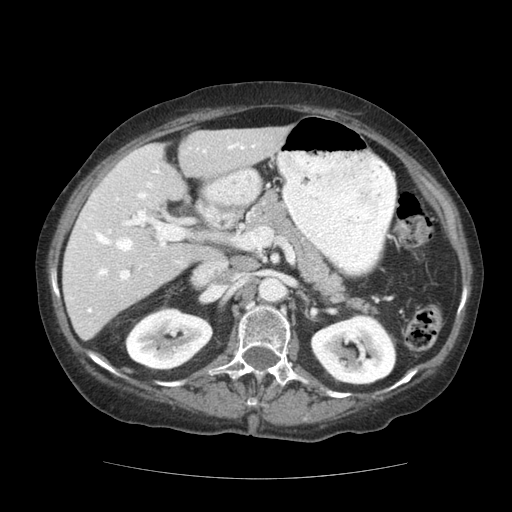
Contrast-enhanced abdominal CT (liver protocol), one axial slice. Position 67 of 111 along the scan axis. 140 kVp. Soft-tissue window (W 400 / L 40 HU). 2.5 mm slice thickness. 512 × 512 image matrix. From the clinical record (not read from this slice): diagnosis: hepatocellular carcinoma (patient treated with transarterial chemoembolisation; whether this scan precedes or follows treatment is not stated here); TNM stage (as recorded): Stage-I; Child-Pugh class: A; tumour size: 7.3 cm.
Annotated regions visible in this slice (semi-automatically segmented with operator editing):
- liver parenchyma outside the tumour (the mass and vessels are separate outlines, so this box may not span the whole liver): bounding box <62,126,288,340> (left, top, right, bottom; pixels)
- liver vessels: <72,143,255,312>